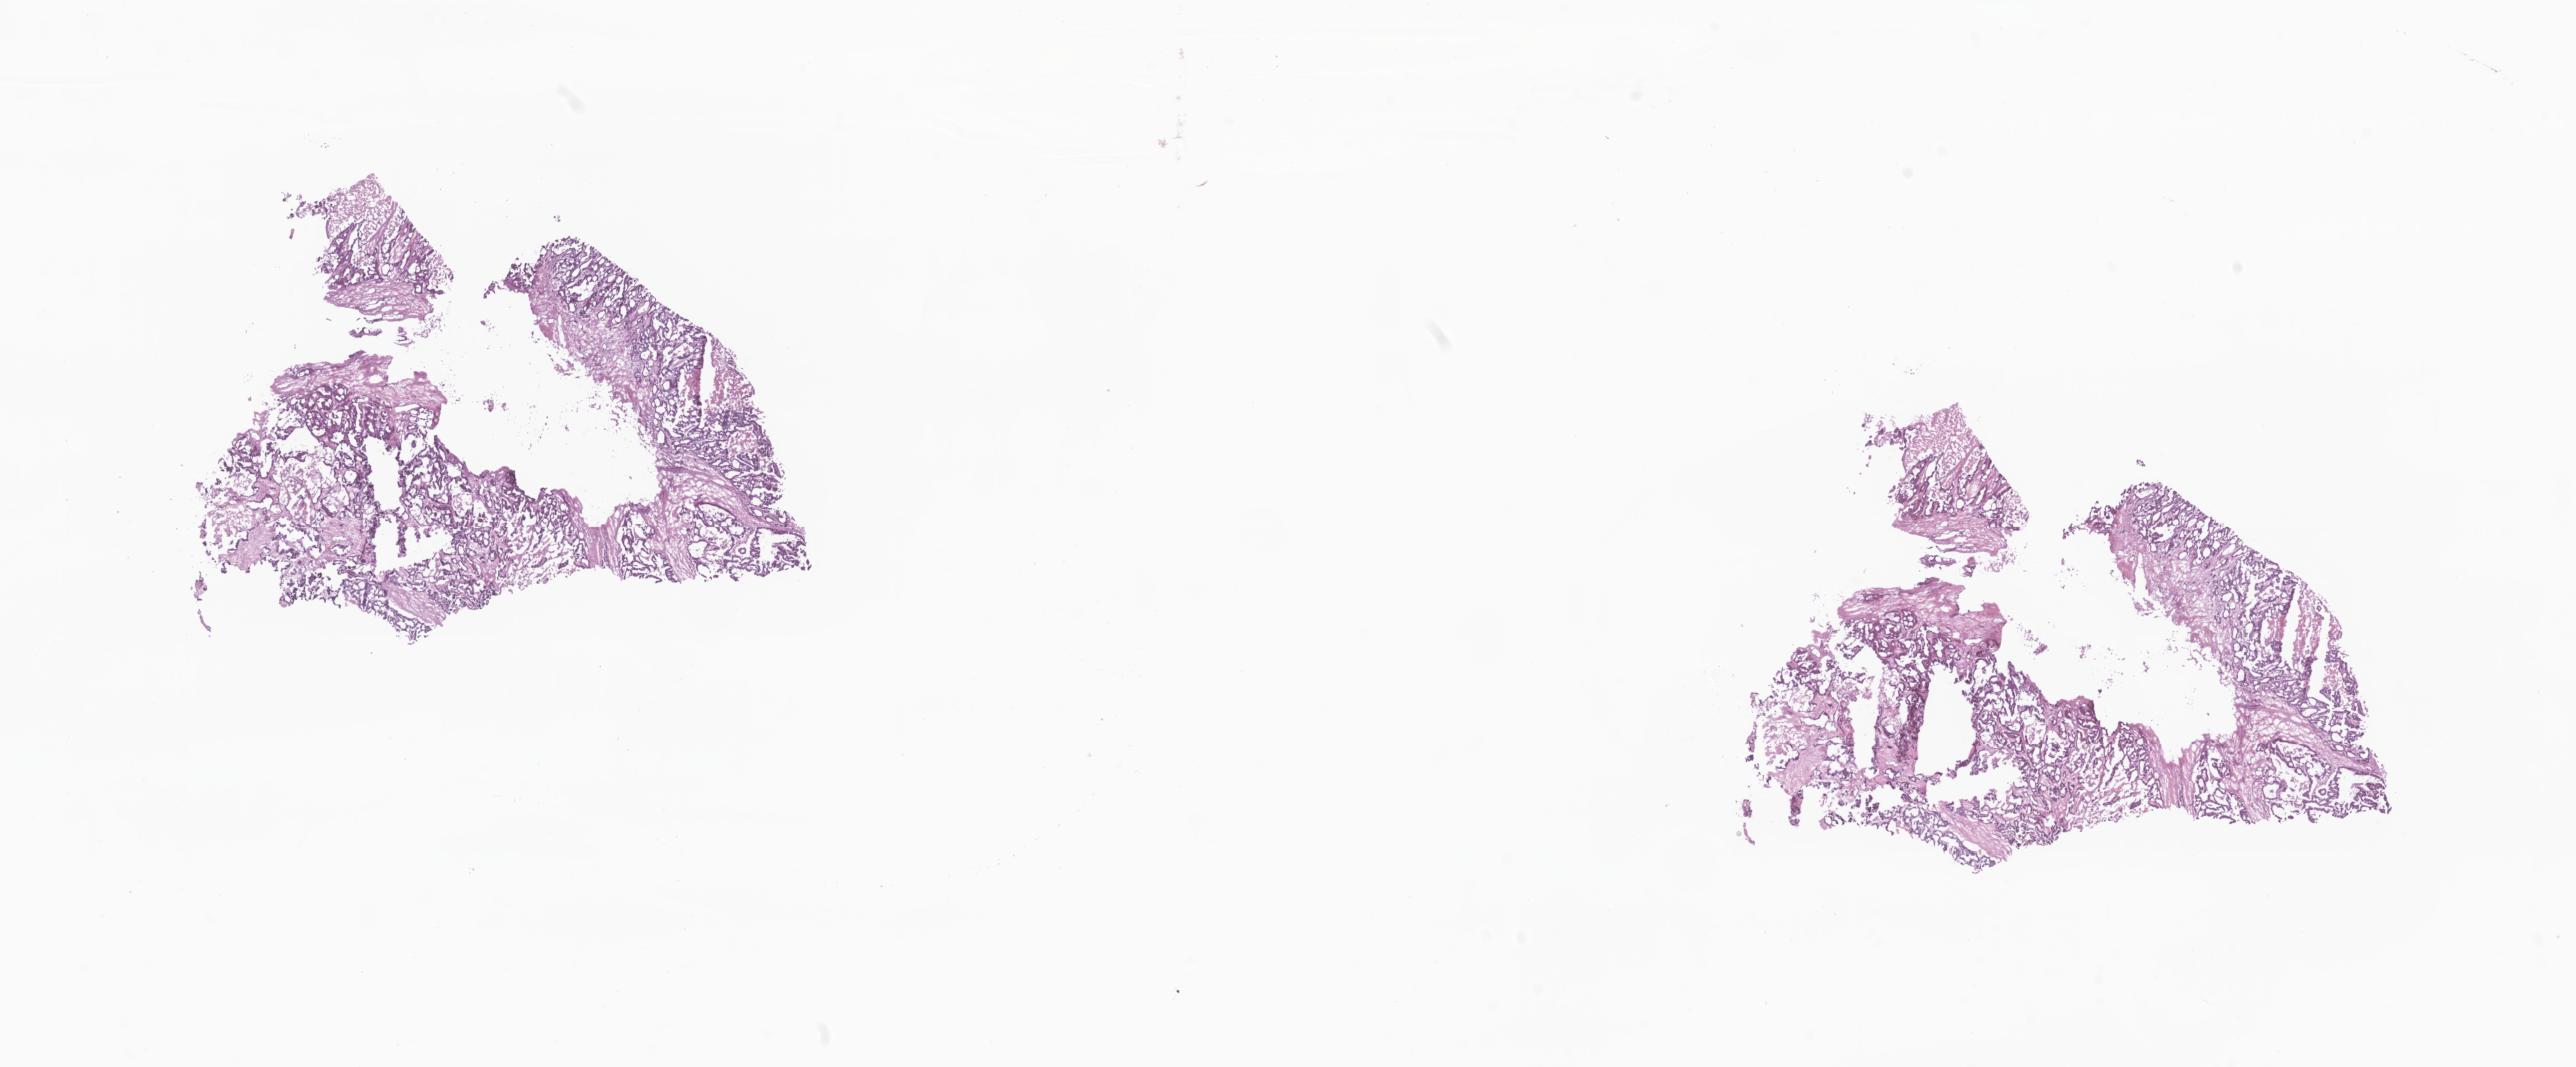
Digitized haematoxylin and eosin-stained section, low-resolution overview of the scanned area, about 25.3 x 10.5 mm, frozen section (tissue freezing medium), metastatic tumor tissue, resected from liver. Male patient; age at initial diagnosis 71 years. Composition of this section per pathologist review: tumor cells 80%, tumor nuclei 80%, stromal cells 15%, necrosis 5%, normal cells 0%. Inflammatory infiltration, as recorded: lymphocyte infiltration 3%, monocyte infiltration 1%, neutrophil infiltration 6%.
Patient diagnosis (primary): Adenocarcinoma, NOS.